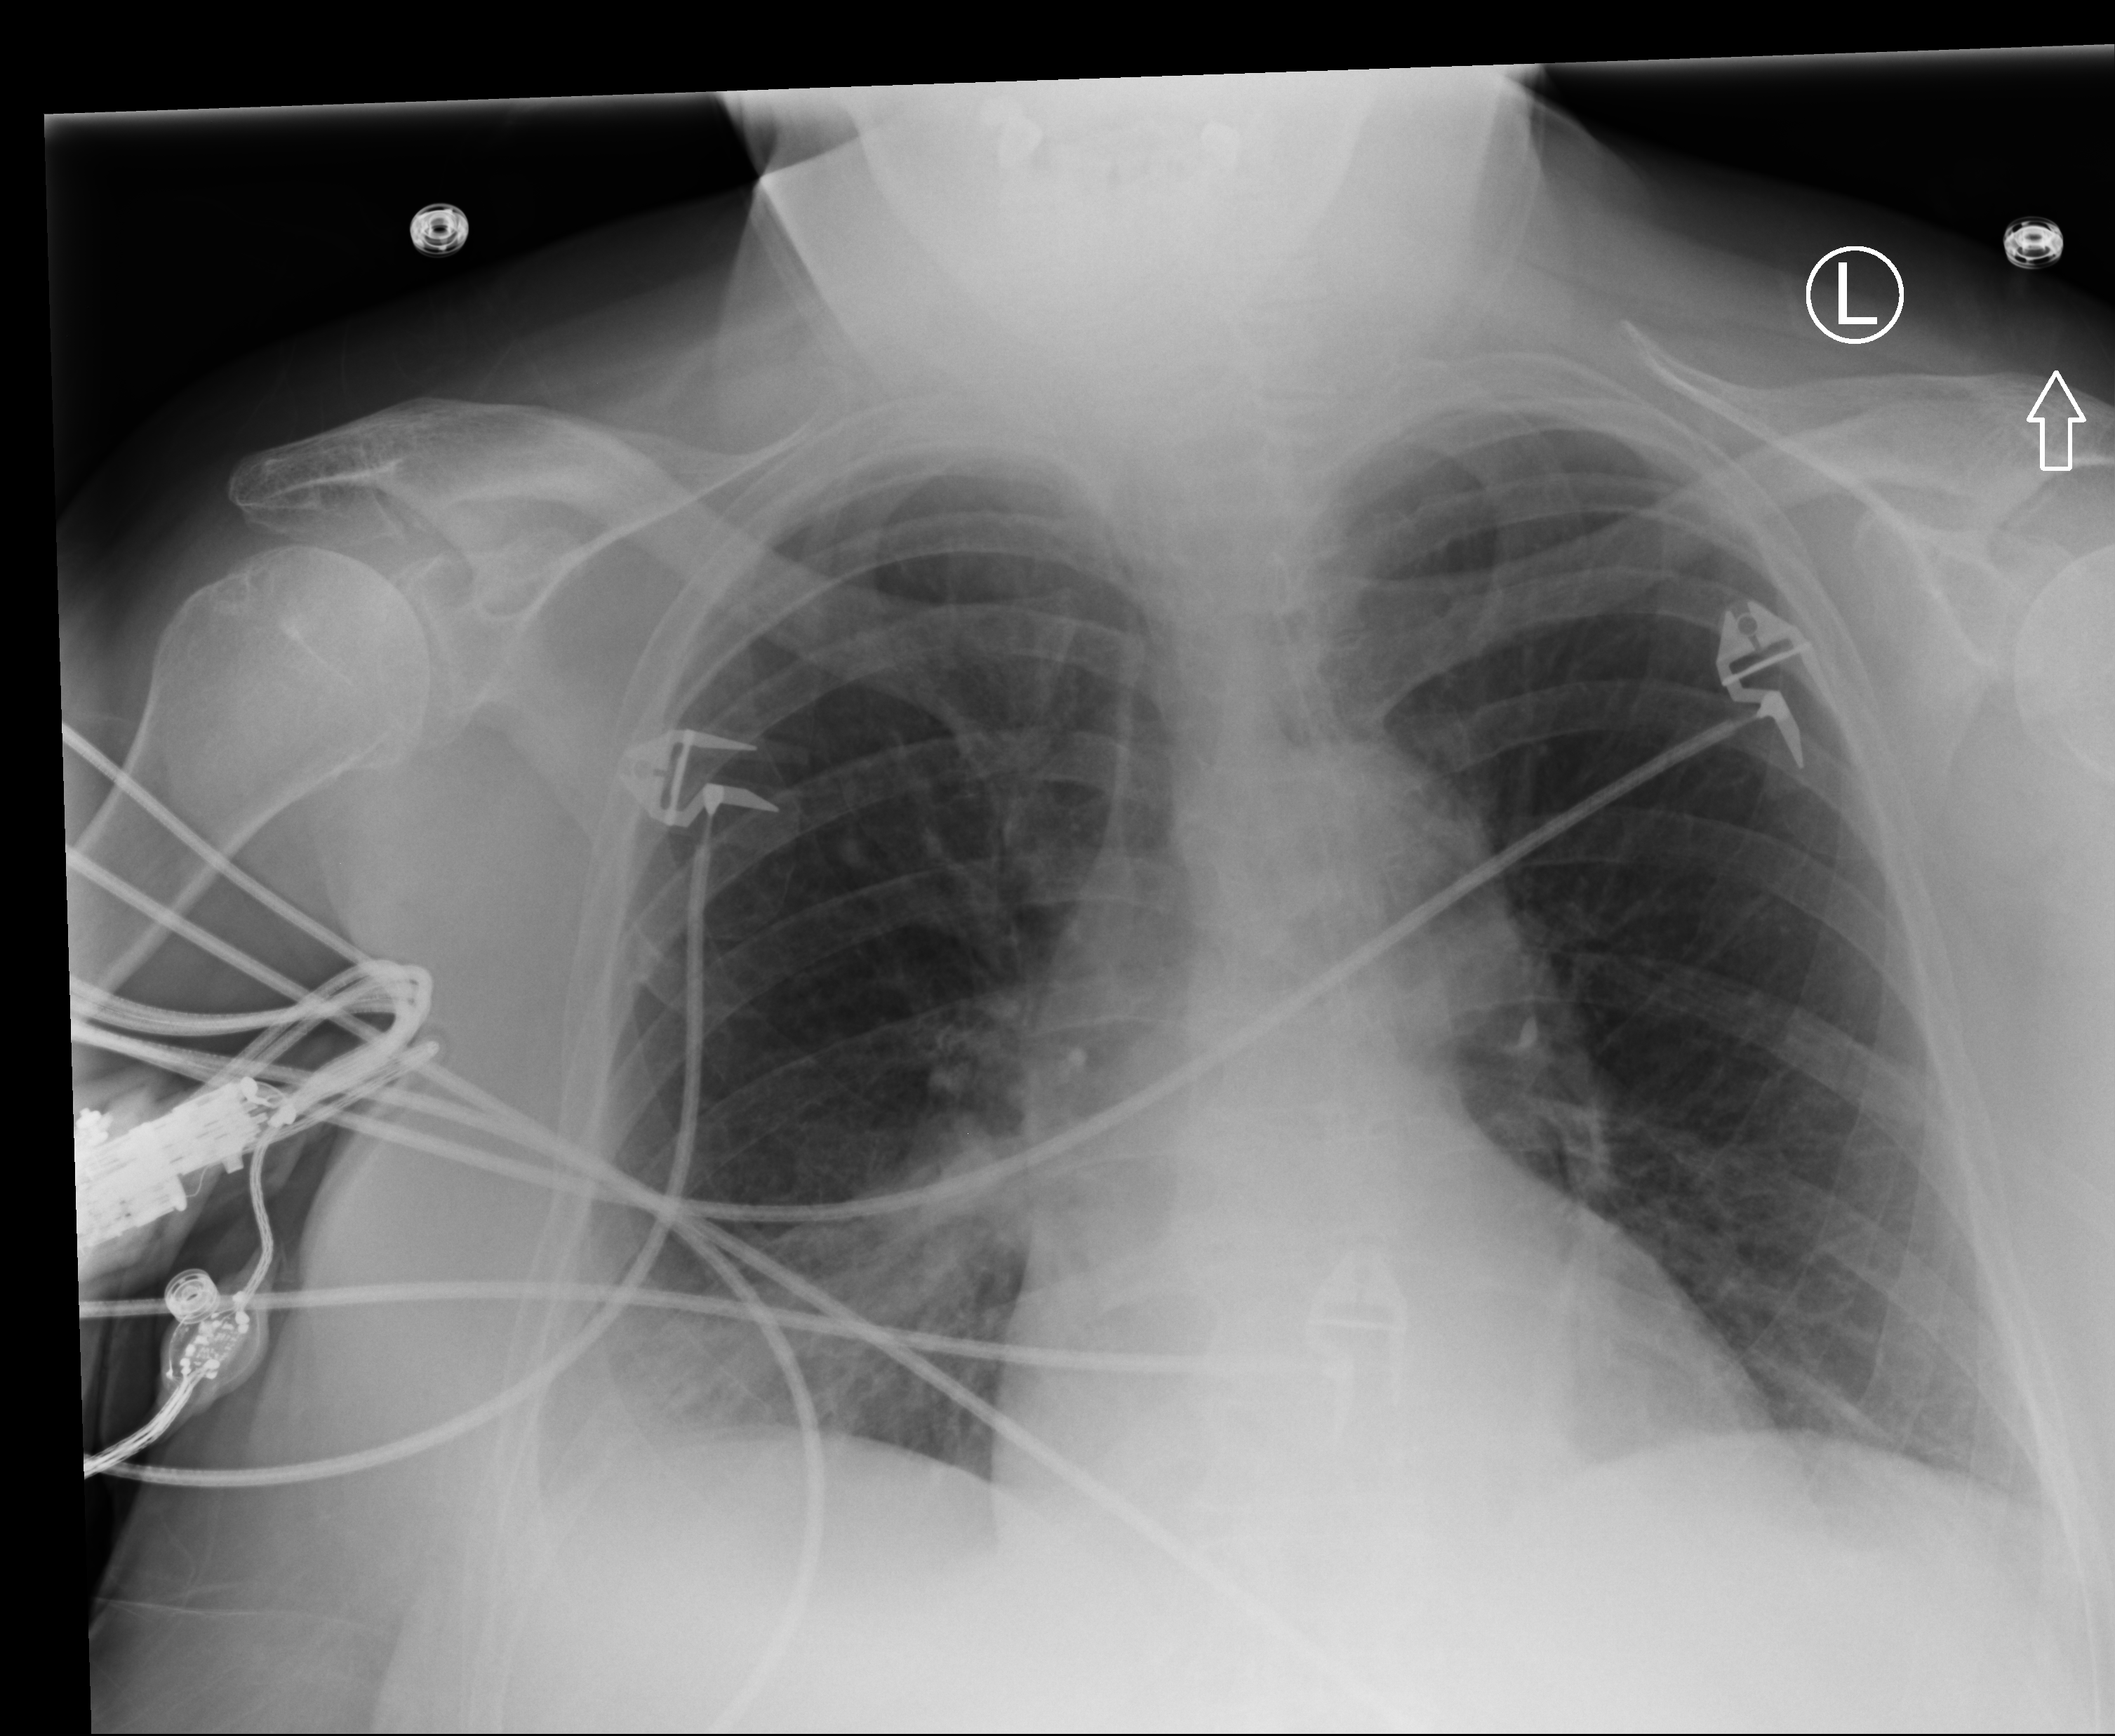
Portable chest radiograph; anteroposterior (AP) projection. Female patient hospitalised with COVID-19, age 75–90 years.
From the hospital-stay record, not from the radiograph (when in the stay this image was taken is not recorded): admitted to intensive care during this hospital stay: no.